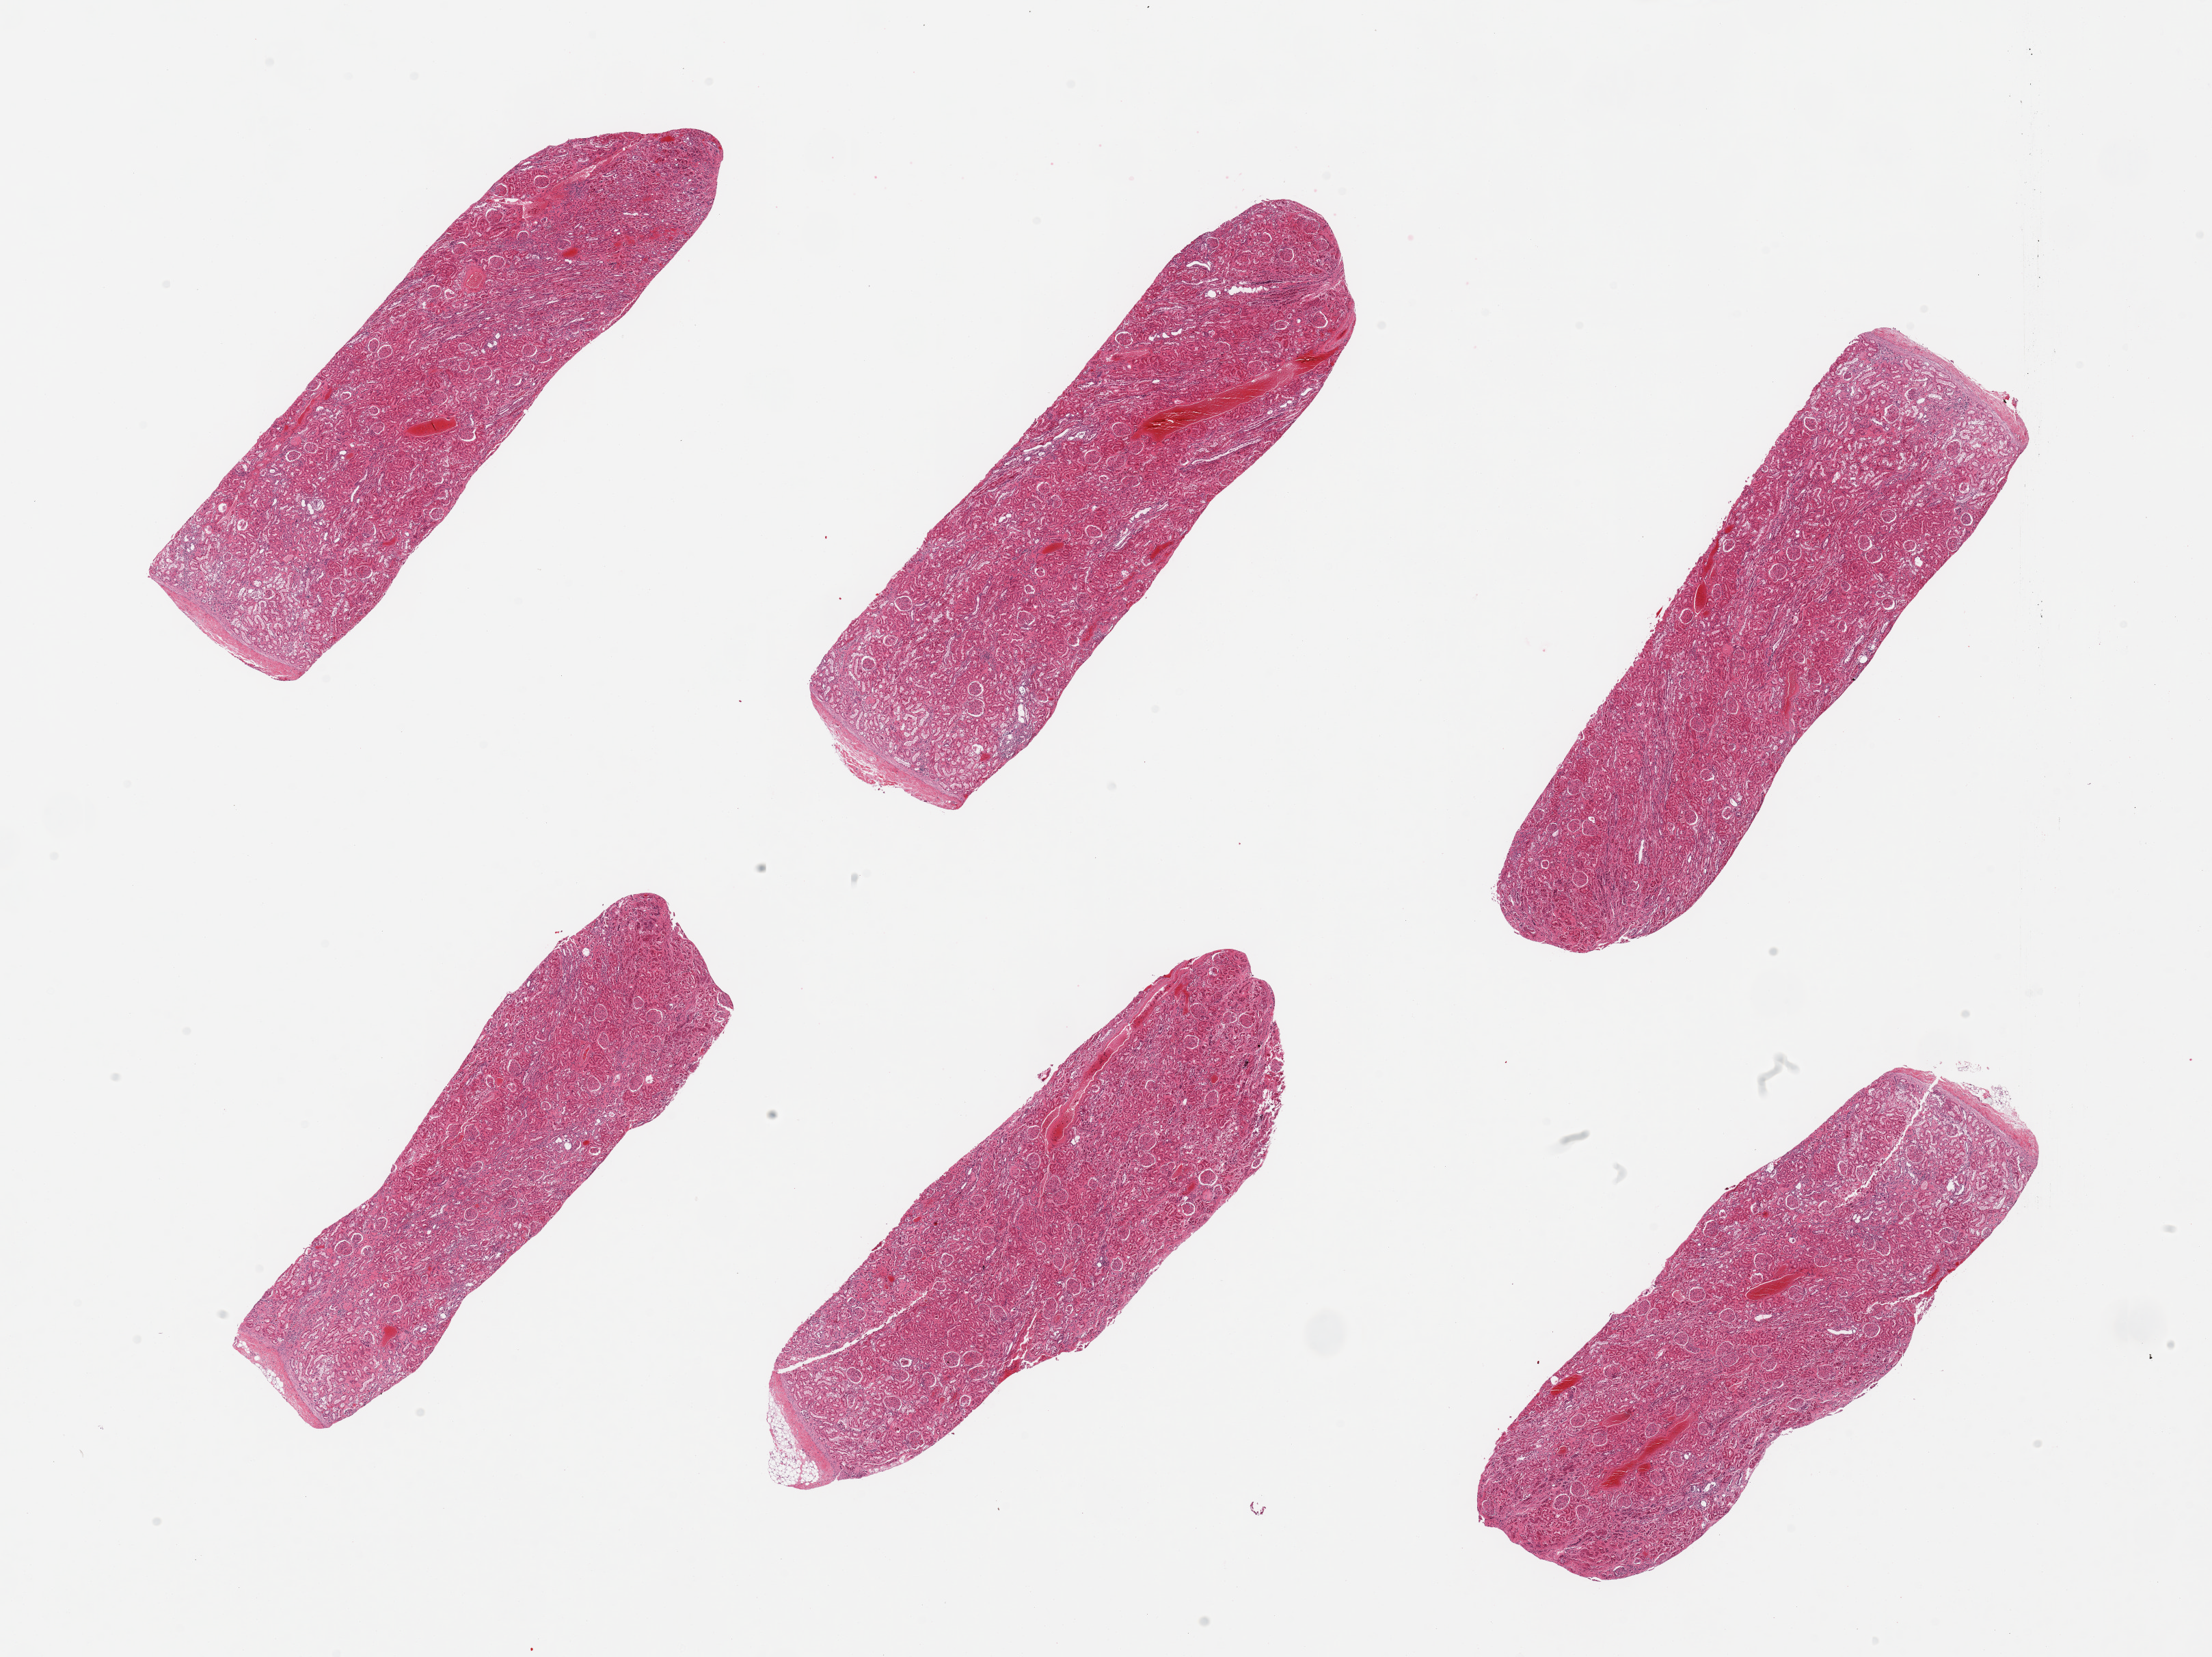
Whole-slide image, haematoxylin and eosin stain — low-resolution overview of the scanned area, about 25.6 x 19.2 mm, PAXgene-fixed paraffin-embedded (PFPE) section, section of renal cortex (target tissue), tissue donor sample. Male donor.
Pathologist's review note for this sample: 6 pieces, glomeruli present, all sections, tubules moderately-markedly autolyzed.